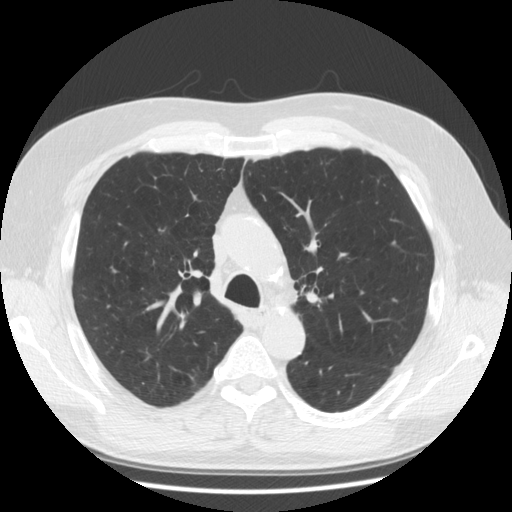
Low-dose screening chest CT, axial slice, second screening round (one year after baseline), lung window (W 1500 / L -600 HU), 2.5 mm slice thickness, standard (soft-tissue) reconstruction kernel (STANDARD), 120 kVp. Male, age 63 years at enrolment. Former smoker at enrolment.
Expert-annotated lung lesion, bounding box [x1, y1, x2, y2] px = [144, 216, 181, 242]. No non-calcified nodule or mass ≥4 mm was recorded by the screening reader at this exam. Lung cancer was diagnosed 717 days after this screen: adenocarcinoma, NOS, right upper lobe, stage IIA (AJCC 6th edition), 8 mm at pathology.